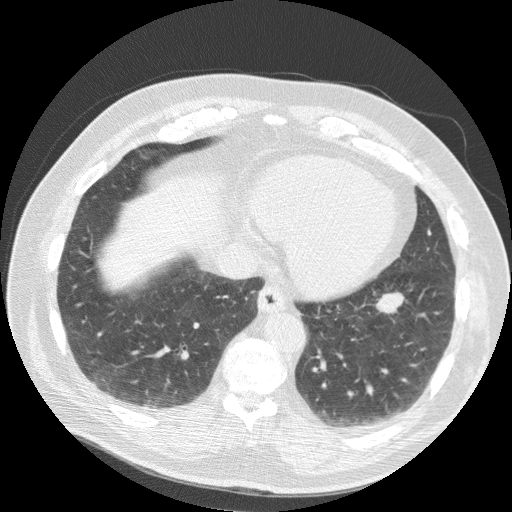
Axial slice from a low-dose chest CT screening exam; second annual screen; lung window (W 1500 / L -600 HU); 2.5 mm slice thickness; standard (soft-tissue) reconstruction kernel (STANDARD); 512 × 512 image matrix, field of view 369 × 369 mm. Male participant, aged 63 years at enrolment. Current smoker at enrolment.
• Expert reader's lesion annotation, bounding box <362,284,410,324> (left, top, right, bottom; pixels).
• The screening reader recorded 2 non-calcified nodules or masses ≥4 mm on this exam (right middle lobe, left lower lobe); which of them this box marks is not recorded.
• Official screen result: positive, change unspecified: nodule(s) >= 4 mm or enlarging nodule(s), mass(es), or other non-specific abnormalities suspicious for lung cancer.